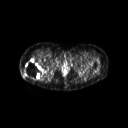
FDG PET of an extremity soft-tissue mass (from a PET/CT study), one axial slice. Position 36 of 267 along the scan axis. 3.27 mm slice thickness. 128 × 128 image matrix. Female patient, age 57 years. Case-level facts recorded for this patient, not image findings: histological type: epithelioid sarcoma with vascular differentiation; site of the primary tumour: right buttock.
Outlined on this slice (expert contour drawn on MRI and transferred to this co-registered scan by the dataset authors):
- gross tumour volume (mass): box from (x=24, y=59) to (x=43, y=79) px